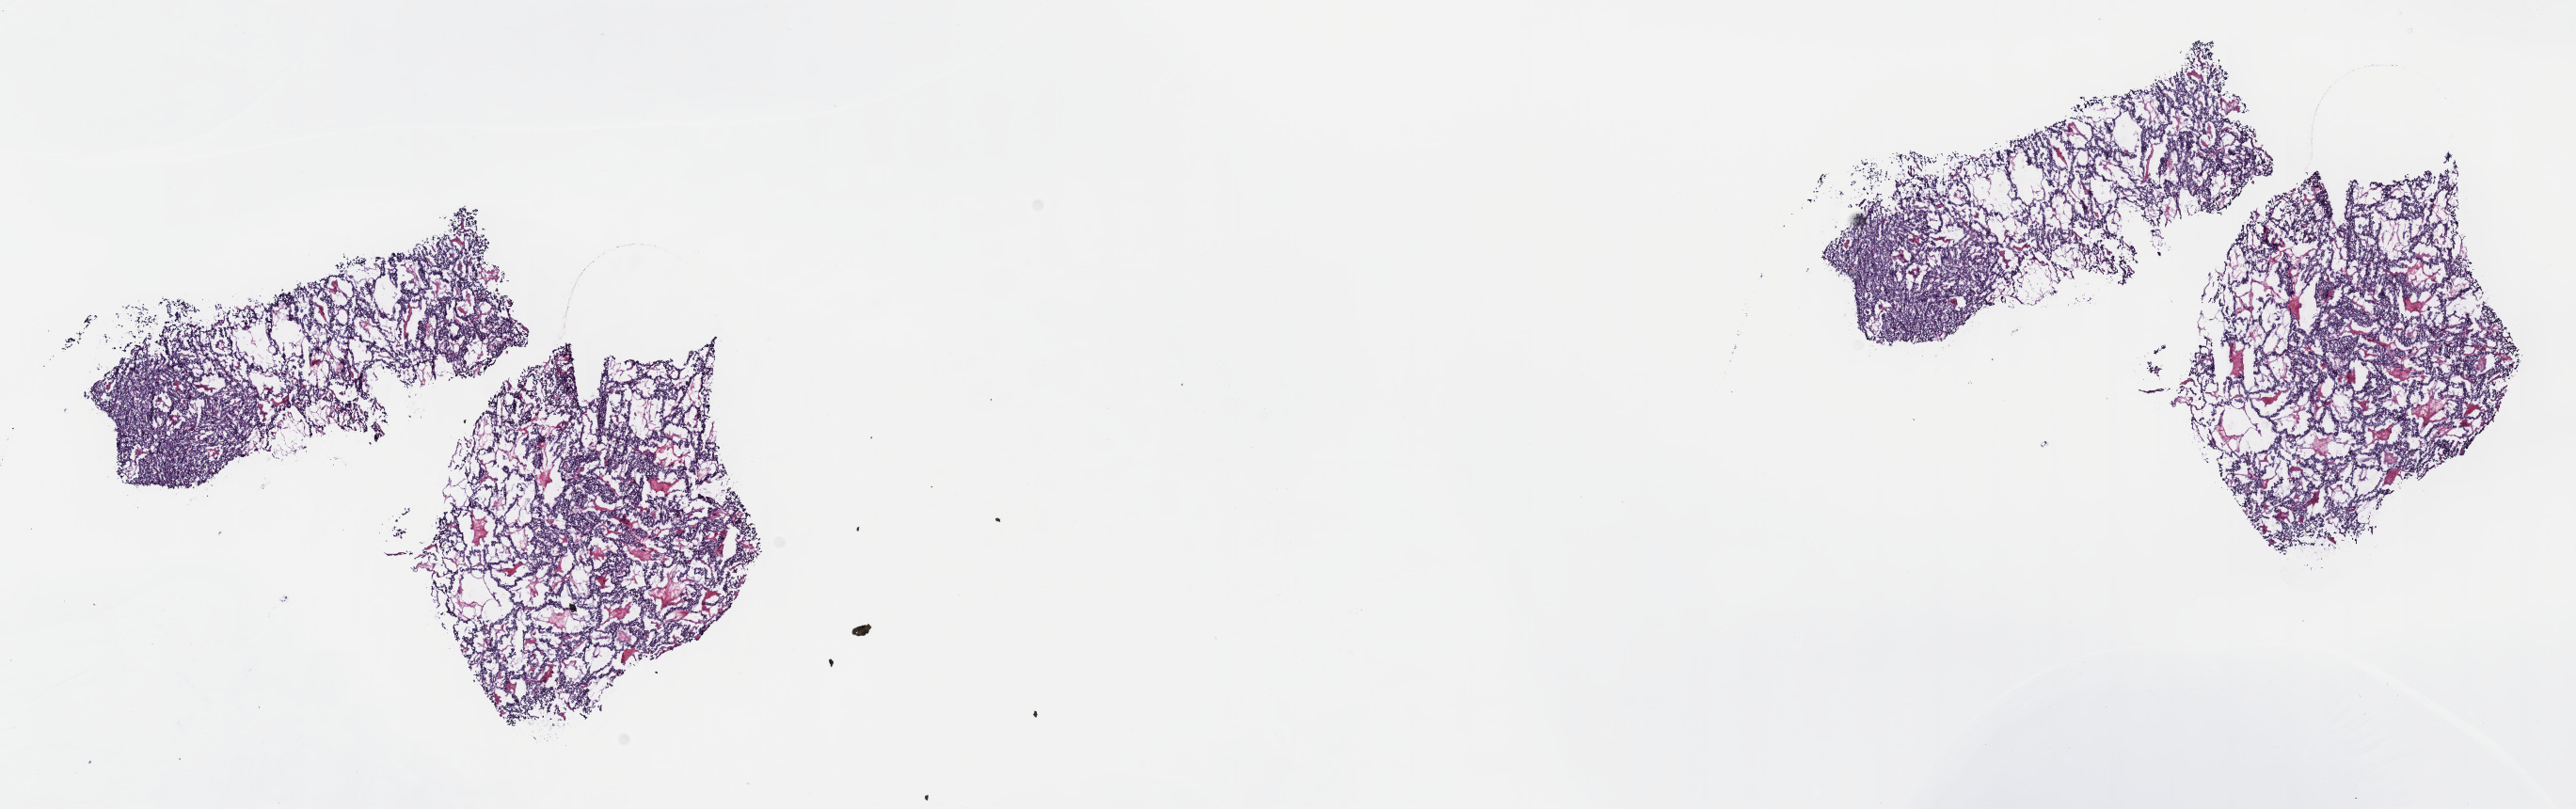
Whole-slide histology image, Hematoxylin and eosin (H&E) stained — shown as a low-resolution overview of the whole scanned area (about 22.1 x 7.0 mm), frozen section from the top of the tissue portion, primary tumour sample from the pancreas. Male, age 67 years at initial diagnosis. Histologic grade: G1 (well differentiated). Pathologist review of this section (percent, as recorded): tumour cells 100%, tumour nuclei 95%, normal cells 0%, stromal cells 0%, necrosis 0%. Inflammatory infiltration, as recorded: lymphocyte infiltration 0%, monocyte infiltration 0%, neutrophil infiltration 0%.
* lymph nodes positive (case pathology): 0 of 32 examined
* AJCC pathologic stage: IB (7th edition)
* pathologic diagnosis: Neuroendocrine carcinoma, NOS (body of pancreas)
* TNM: T2 N0 MX